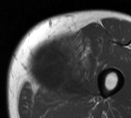
MRI of an extremity soft-tissue mass, one axial slice. Slice 19 of 55 in the series (ordered by position). MR volume resampled by the dataset authors to the PET/CT grid (not the native acquisition matrix). 131 × 118 image matrix, field of view 128 × 115 mm. Male patient. From the clinical record (not read from this slice): histological type: pleiomorphic liposarcoma; grade: high; site of the primary tumour: left thigh.
Annotated regions visible in this slice (expert contour drawn on MRI and transferred to this co-registered scan by the dataset authors):
- gross tumour volume including surrounding oedema: bounding box [x1, y1, x2, y2] px = [27, 36, 94, 101]
- gross tumour volume (mass): [27, 37, 76, 92]